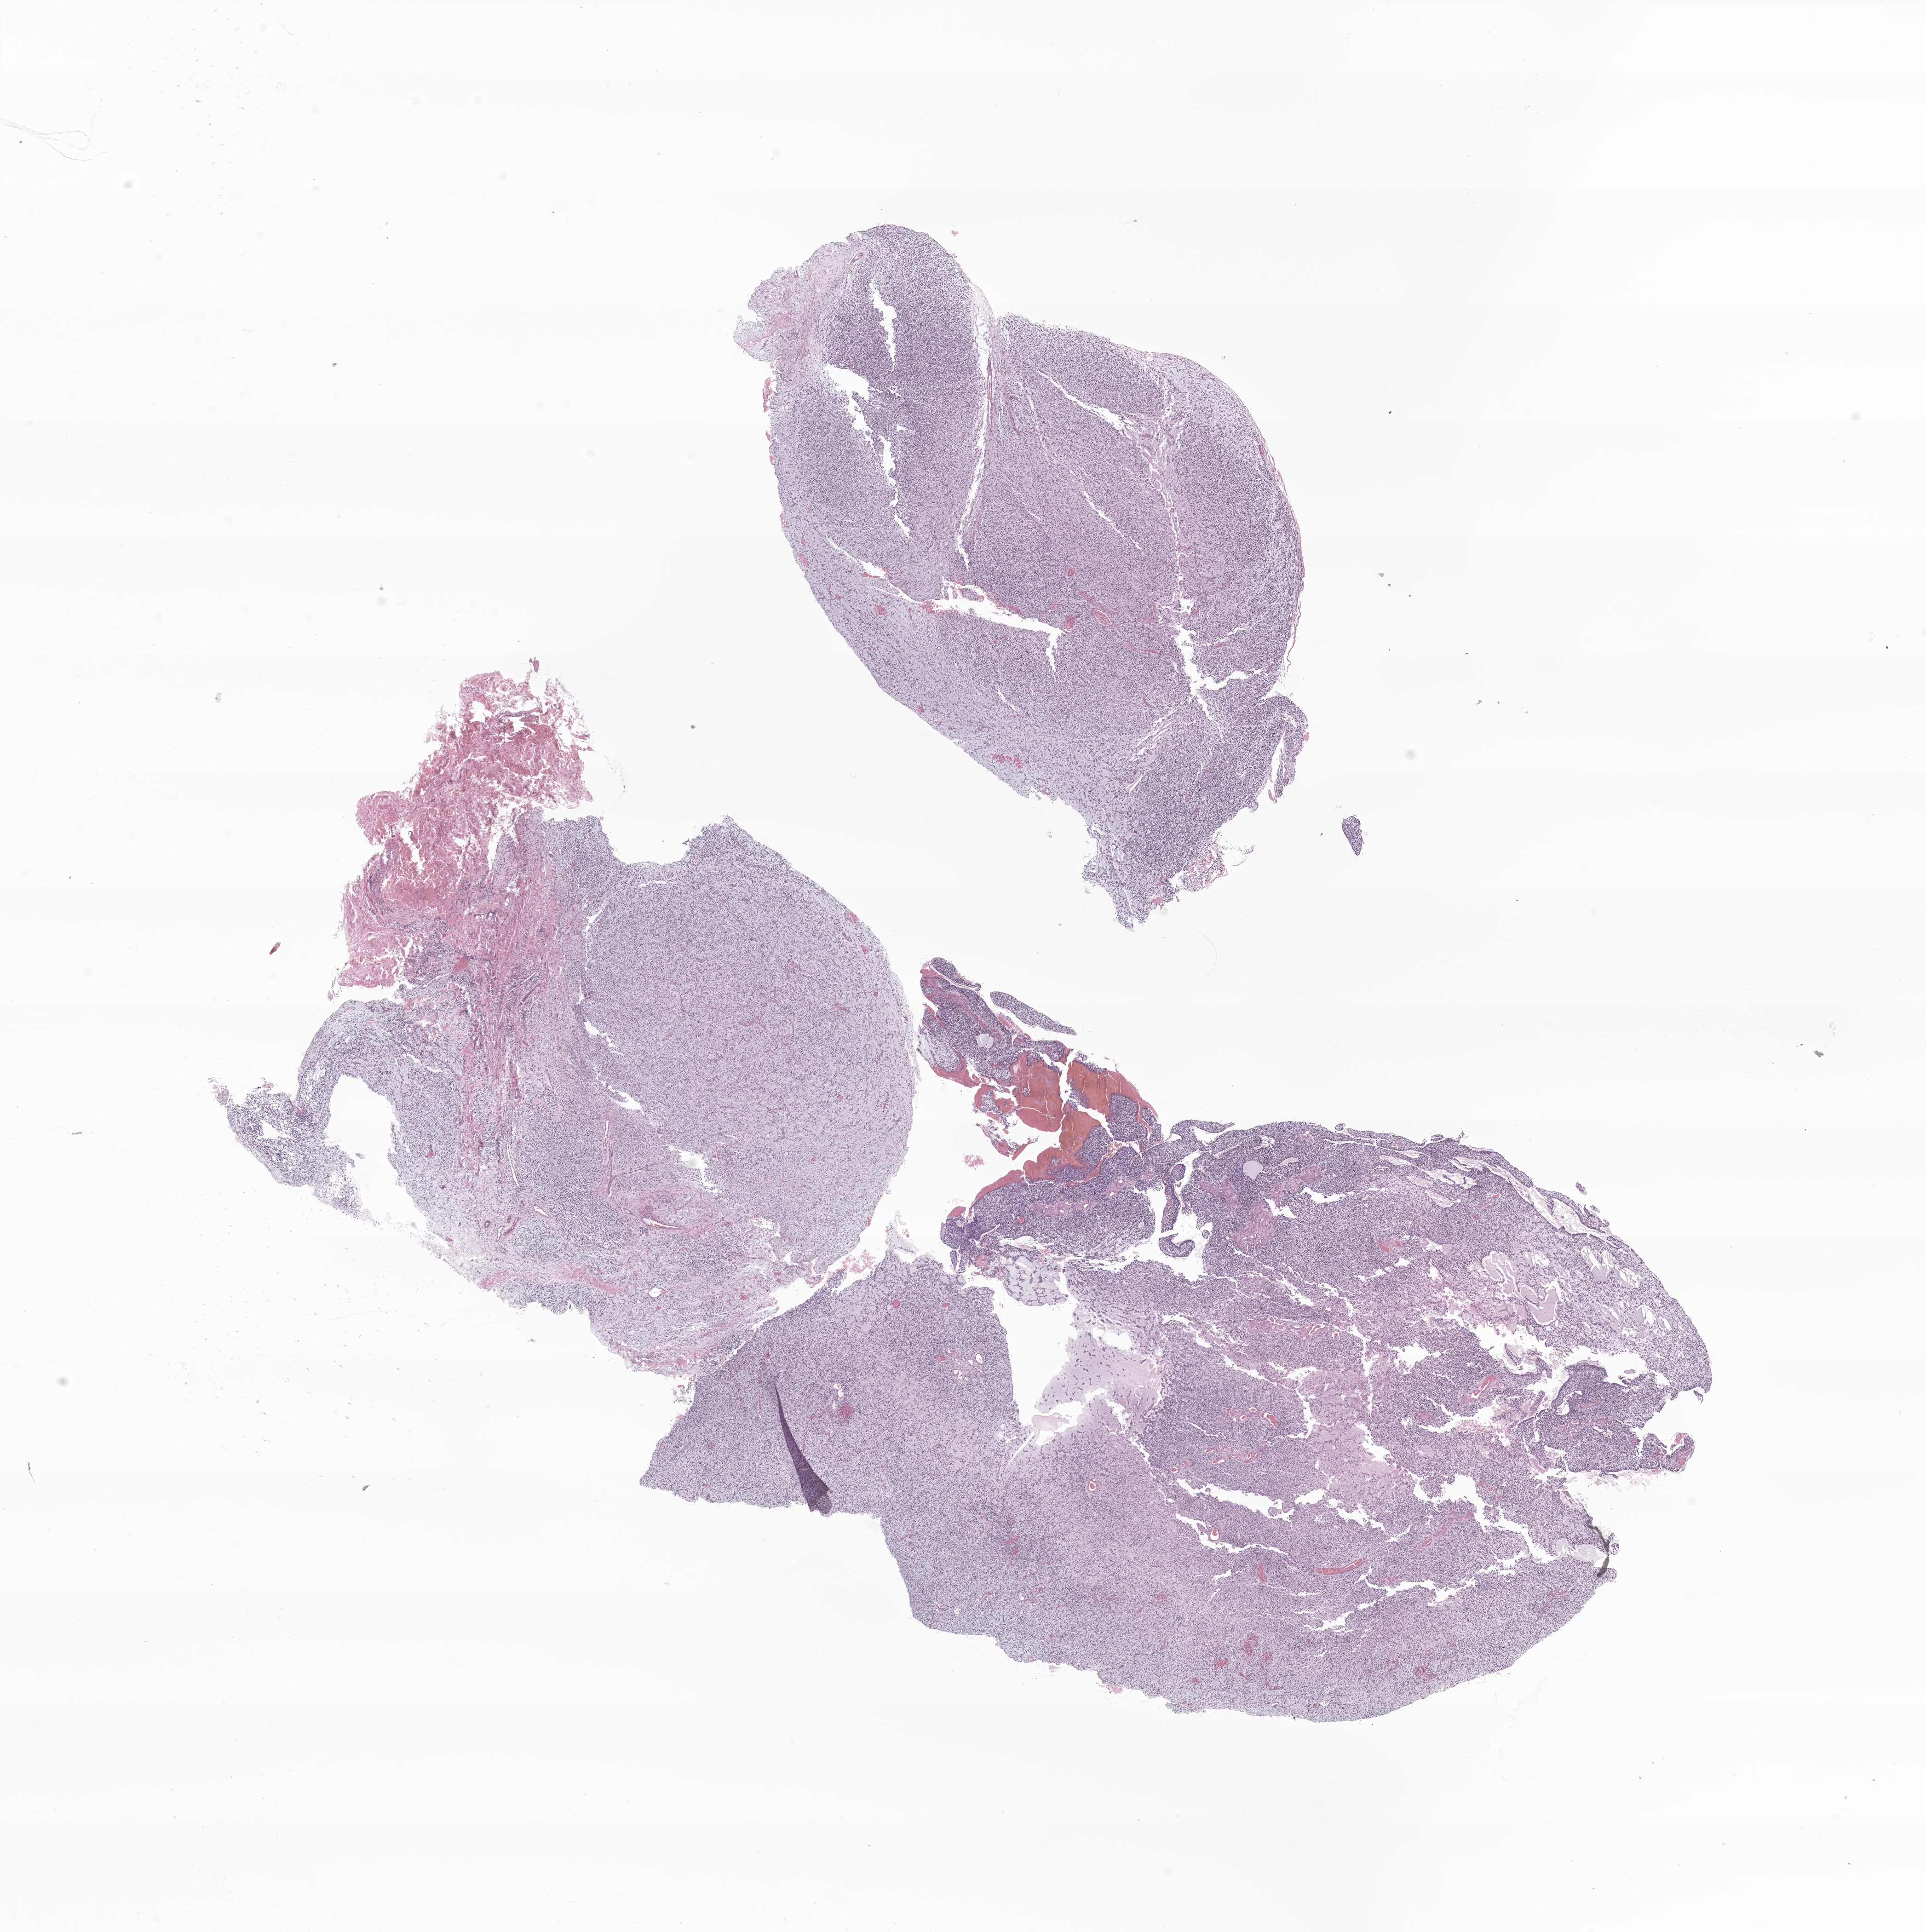
Digitized H&E-stained section of tumor tissue from the soft tissues of head and neck, shown as a low-resolution overview of the whole scanned area (about 17.7 x 17.7 mm). Formalin-fixed, paraffin-embedded (FFPE) tissue. Patient: male, age 88 months (7 years 4 months).
Recorded diagnosis: Embryonal rhabdomyosarcoma, NOS. Tissue or organ of origin (case record): connective, subcutaneous and other soft tissues of head, face, and neck.